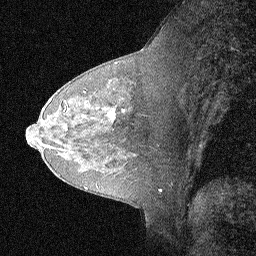
Breast MRI (dynamic contrast-enhanced), one sagittal slice; position 39 of 64 along the scan axis; dynamic contrast-enhanced study with each time point stored as its own series, time point 2 of 3 at this slice position (early post-contrast, ordered by acquisition time); 1.5 T; TE 4.5 ms, TR 11 ms; 2.06 mm slice thickness; 256 × 256 image matrix, field of view 200 × 200 mm. Female patient, age 62 years. Case-level facts recorded for this patient, not image findings: setting: breast cancer imaged before/during neoadjuvant chemotherapy; receptor status: HR-positive, HER2-negative.
Structures marked on this image (semi-automatically segmented with operator editing):
- analysis volume of interest (the breast-tissue region the enhancement analysis was run in; not a lesion): bounding box [x1, y1, x2, y2] px = [91, 93, 124, 129]
- tumour enhancement mask (voxels above the 90 % enhancement threshold inside the analysis volume of interest): [106, 111, 115, 120]